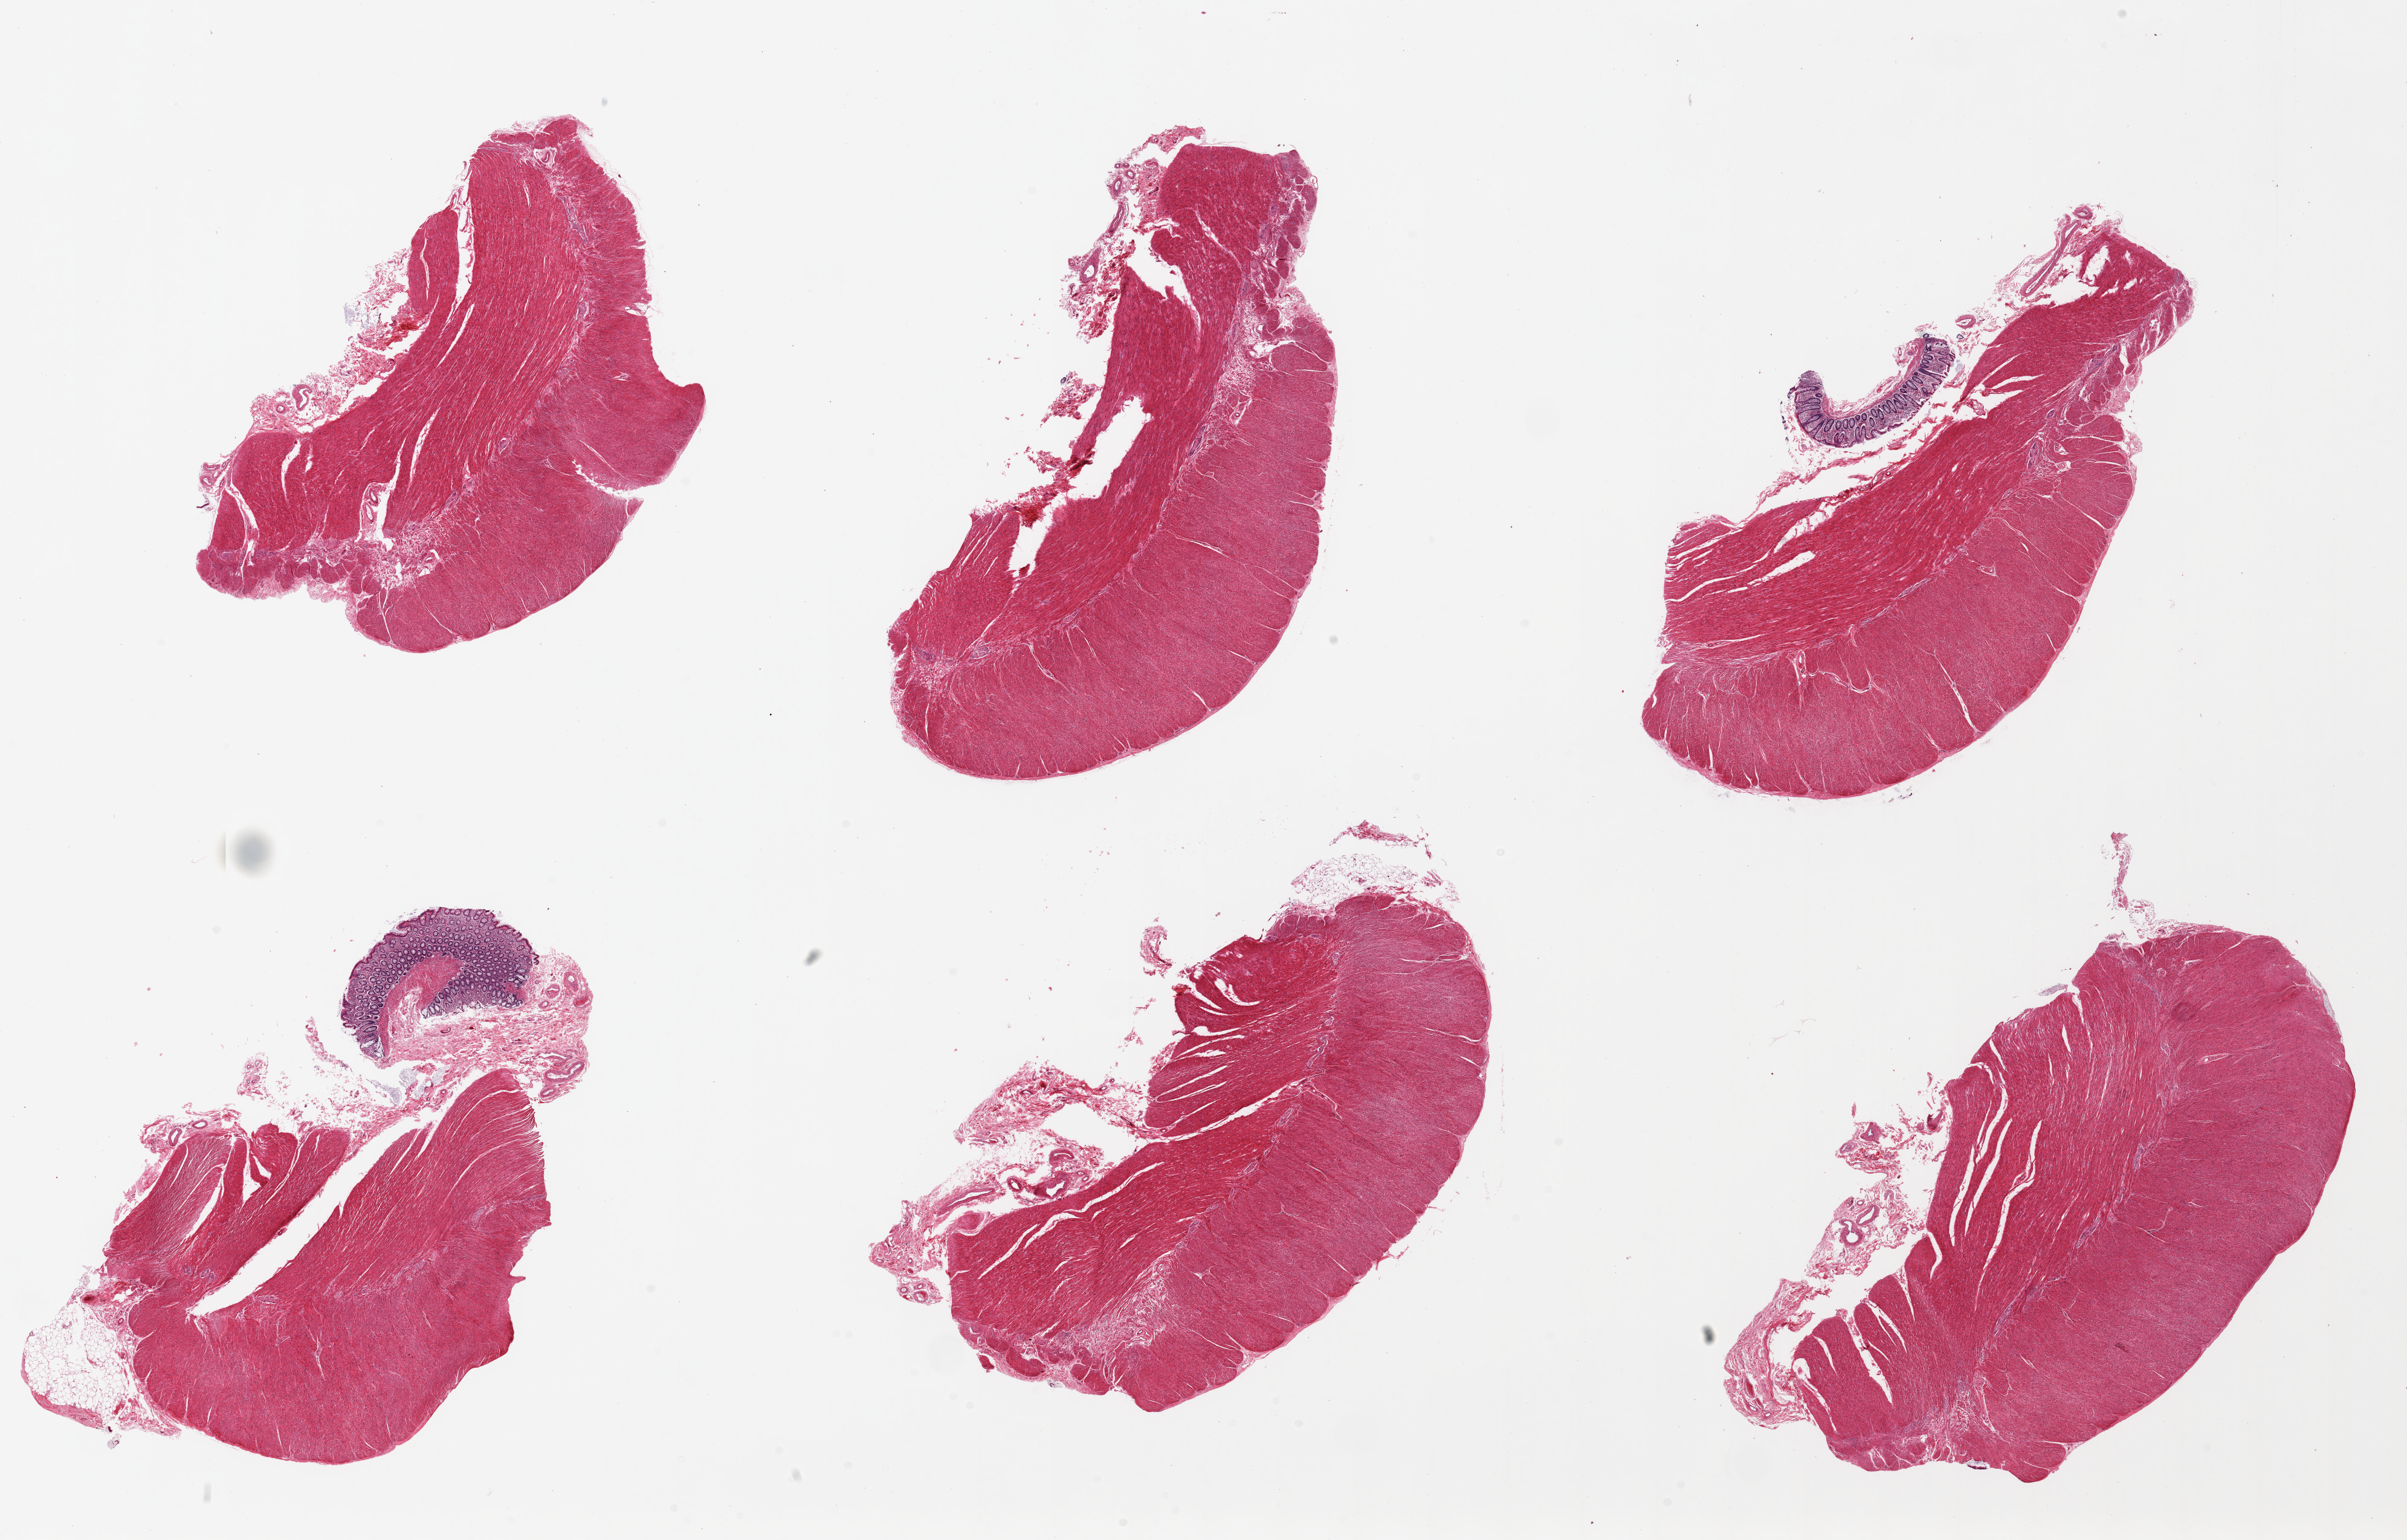
Digitized hematoxylin and eosin (H&E)-stained section — shown as a low-resolution overview of the whole scanned area (about 31.5 x 20.2 mm); PAXgene-fixed paraffin-embedded (PFPE) section; section of sigmoid colon (target tissue); donor tissue sample. Donor sex: male.
Pathologist's review note for this sample: 6 pieces. 2 pieces have mucosal remnants [not target].